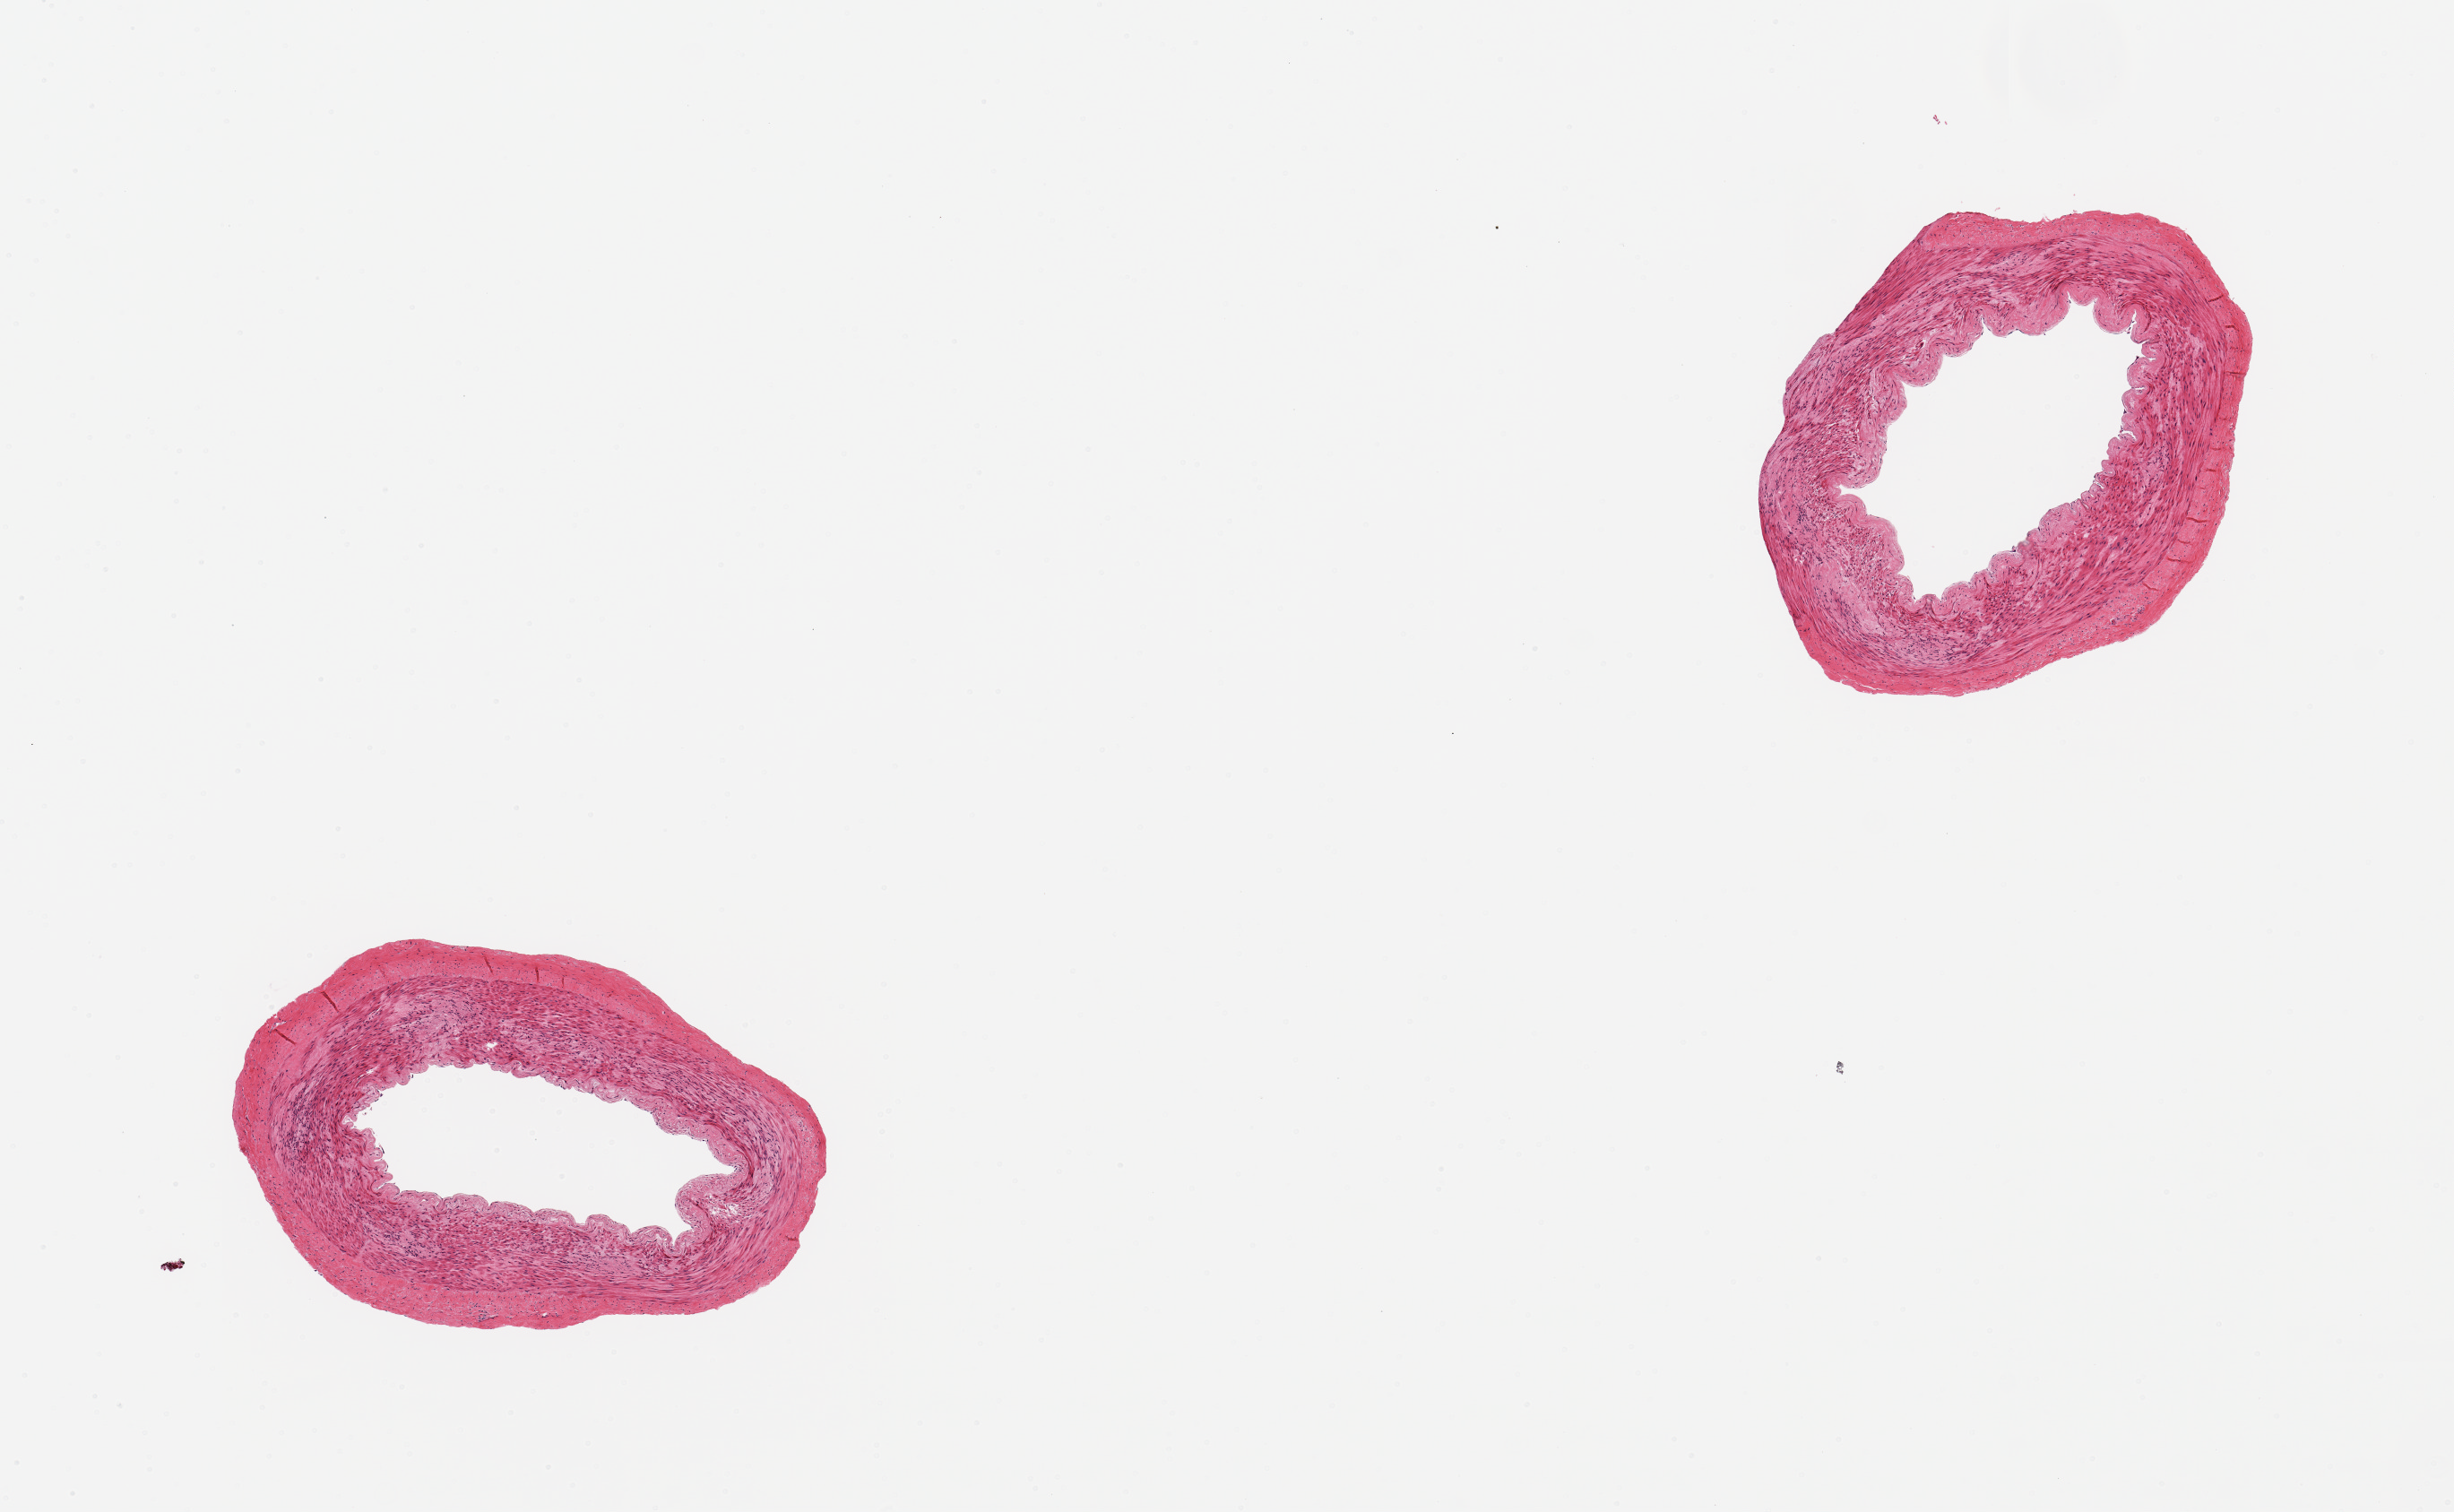
H&E whole-slide image, brightfield, whole scanned area (about 10.8 x 6.7 mm) shown as a low-resolution overview. PAXgene-fixed, paraffin-embedded tissue. Section of tibial artery (target tissue). Tissue donor sample. Donor sex: male.
Reviewer comment on this tissue sample: 2 pieces, clean specimens, no adherent fat.